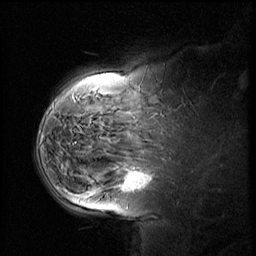
Breast MRI (dynamic contrast-enhanced), one sagittal slice; slice 42 of 58 in the series (ordered by position); dynamic contrast-enhanced series, image 2 of 2 at this slice position (ordered by acquisition); 1.5 T; TE 4.2 ms, TR 8.9 ms; 3 mm slice thickness; 256 × 256 image matrix, field of view 220 × 220 mm. Female patient, age 37 years. Case-level facts recorded for this patient, not image findings: setting: breast cancer imaged before/during neoadjuvant chemotherapy; receptor status: triple-negative.
Annotated regions visible in this slice (semi-automatically segmented with operator editing):
- analysis volume of interest (the breast-tissue region the enhancement analysis was run in; not a lesion): box from (x=114, y=160) to (x=166, y=207) px
- tumour enhancement mask (voxels above the 140 % enhancement threshold inside the analysis volume of interest): (x=124, y=174)–(x=149, y=189)